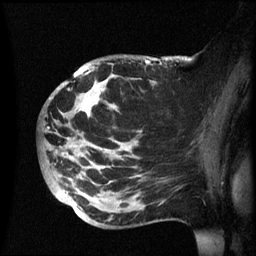
Breast MRI (dynamic contrast-enhanced), one sagittal slice; position 36 of 60 along the scan axis; dynamic contrast-enhanced series, image 2 of 3 at this slice position (ordered by acquisition); 1.5 T; TE 4.2 ms, TR 8.4 ms; 2.4 mm slice thickness; 256 × 256 image matrix. Female patient, age 49 years.
Outlined on this slice (semi-automatically segmented with operator editing):
- analysis volume of interest (the breast-tissue region the enhancement analysis was run in; not a lesion): bounding box <41,55,174,228> (left, top, right, bottom; pixels)
- tumour enhancement mask (voxels above the 70 % enhancement threshold inside the analysis volume of interest): <82,60,146,150>